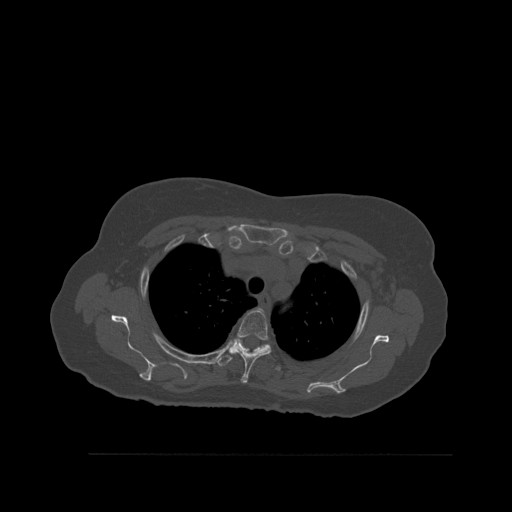
CT including the spine, one axial slice; position 417 of 527 along the scan axis; bone window (W 1800 / L 400 HU); 1.5 mm slice thickness; 512 × 512 image matrix. Patient: female, 73 years. Case-level facts recorded for this patient, not image findings: primary cancer: breast; vertebrae with lytic lesions (as recorded): L2.
Structures marked on this image (semi-automatically segmented with operator editing):
- T2 vertebra: box from (x=258, y=308) to (x=261, y=310) px
- T3 vertebra: (x=231, y=310)–(x=271, y=384)
- T4 vertebra: (x=217, y=349)–(x=281, y=371)